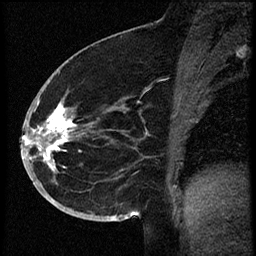
Breast MRI (dynamic contrast-enhanced), one sagittal slice; position 33 of 60 along the scan axis; dynamic contrast-enhanced study with each time point stored as its own series, time point 2 of 3 at this slice position (early post-contrast, ordered by acquisition time); 1.5 T; TE 4.2 ms, TR 18.9 ms; 2 mm slice thickness; 256 × 256 image matrix, field of view 200 × 200 mm. Female patient. From the clinical record (not read from this slice): setting: breast cancer imaged before/during neoadjuvant chemotherapy; receptor status: HR-positive, HER2-negative.
Structures marked on this image (semi-automatically segmented with operator editing):
- analysis volume of interest (the breast-tissue region the enhancement analysis was run in; not a lesion): box from (x=30, y=87) to (x=114, y=173) px
- tumour enhancement mask (voxels above the 100 % enhancement threshold inside the analysis volume of interest): (x=30, y=104)–(x=77, y=166)